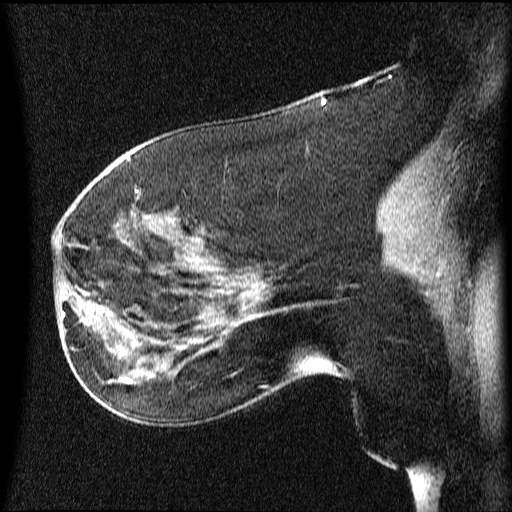
Breast MRI (dynamic contrast-enhanced), one sagittal slice. Position 32 of 64 along the scan axis. Dynamic contrast-enhanced series, image 2 of 4 at this slice position (ordered by acquisition). 1.5 T. TE 4.2 ms, TR 9 ms. 2 mm slice thickness. 512 × 512 image matrix, field of view 200 × 200 mm. Female patient, age 63 years.
Annotated regions visible in this slice (semi-automatic segmentation, software-assisted and operator-edited):
- analysis volume of interest (the breast-tissue region the enhancement analysis was run in; not a lesion): bounding box (x1, y1, x2, y2) in pixels: (66, 274, 131, 353)
- tumour enhancement mask (voxels above the 70 % enhancement threshold inside the analysis volume of interest): (78, 292, 129, 351)